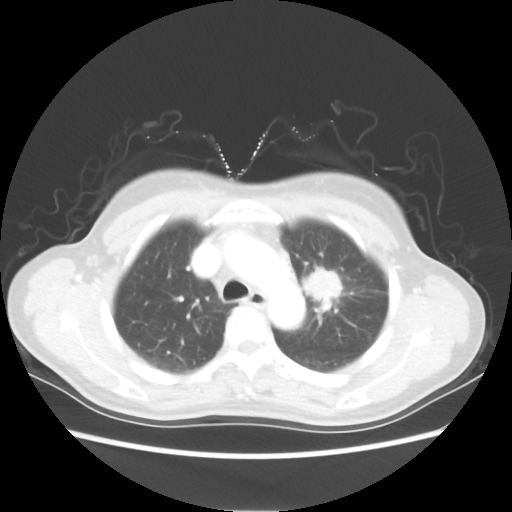
Chest CT, one axial slice; slice 40 of 54 in the series (ordered by position); reconstruction kernel STANDARD; lung window (W 1500 / L -600 HU); 512 × 512 image matrix, field of view 360 × 360 mm. Patient: female, 53 years. From the clinical record (not read from this slice): clinical TNM (as recorded): T1c N0 M0.
Structures marked on this image (bounding box drawn by a radiologist):
- lung tumour (recorded histology: adenocarcinoma): bounding box [x1, y1, x2, y2] px = [298, 260, 342, 306]
- lung tumour (recorded histology: adenocarcinoma): [301, 265, 348, 312]